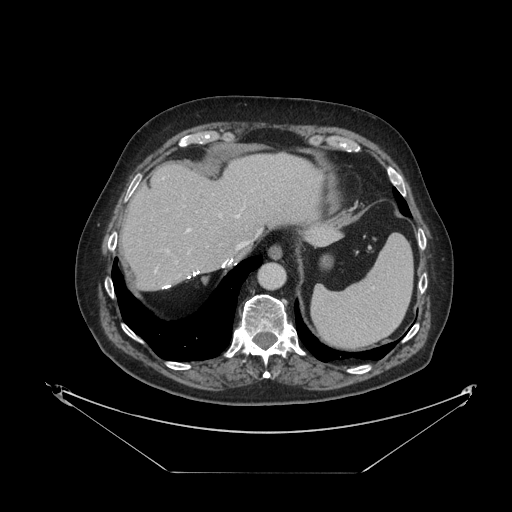
Contrast-enhanced abdominal CT, one axial slice; position 93 of 121 along the scan axis; reconstruction kernel STANDARD; 120 kVp; intravenous contrast given; soft-tissue window (W 400 / L 40 HU); 512 × 512 image matrix, field of view 500 × 500 mm. Male patient, age 68 years. Case-level facts recorded for this patient, not image findings: diagnosis: colorectal cancer liver metastases, imaged before liver resection; multiple liver metastases: no.
Annotated regions visible in this slice (manually delineated by an expert):
- hepatic veins: bounding box (x1, y1, x2, y2) in pixels: (156, 214, 260, 270)
- liver: (122, 153, 337, 290)
- planned liver remnant (the part of the liver to remain after resection): (122, 153, 336, 289)
- portal vein (with intrahepatic branches): (166, 214, 222, 264)